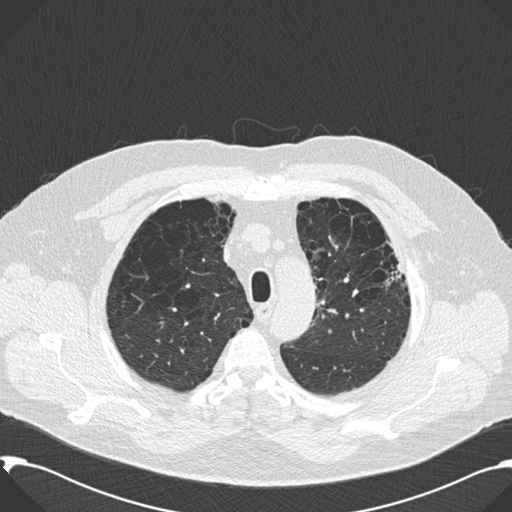
Chest CT (low-dose screening protocol), one axial image. Second annual screen. Lung window (W 1500 / L -600 HU). 2 mm slice thickness. Standard (soft-tissue) reconstruction kernel (B30f). Slice 35 of 199 in the series. Male participant, aged 59 years at enrolment. Current smoker at enrolment.
Expert-annotated lung lesion, bounding box [x1, y1, x2, y2] px = [366, 237, 412, 304]. Screening reader's record for this exam: no non-calcified nodule ≥4 mm recorded. Lung cancer was diagnosed 518 days after this screen (after the third annual screen): bronchiolo-alveolar carcinoma, mixed mucinous and non-mucinous, left upper lobe, stage IA (AJCC 6th edition), 20 mm at pathology.